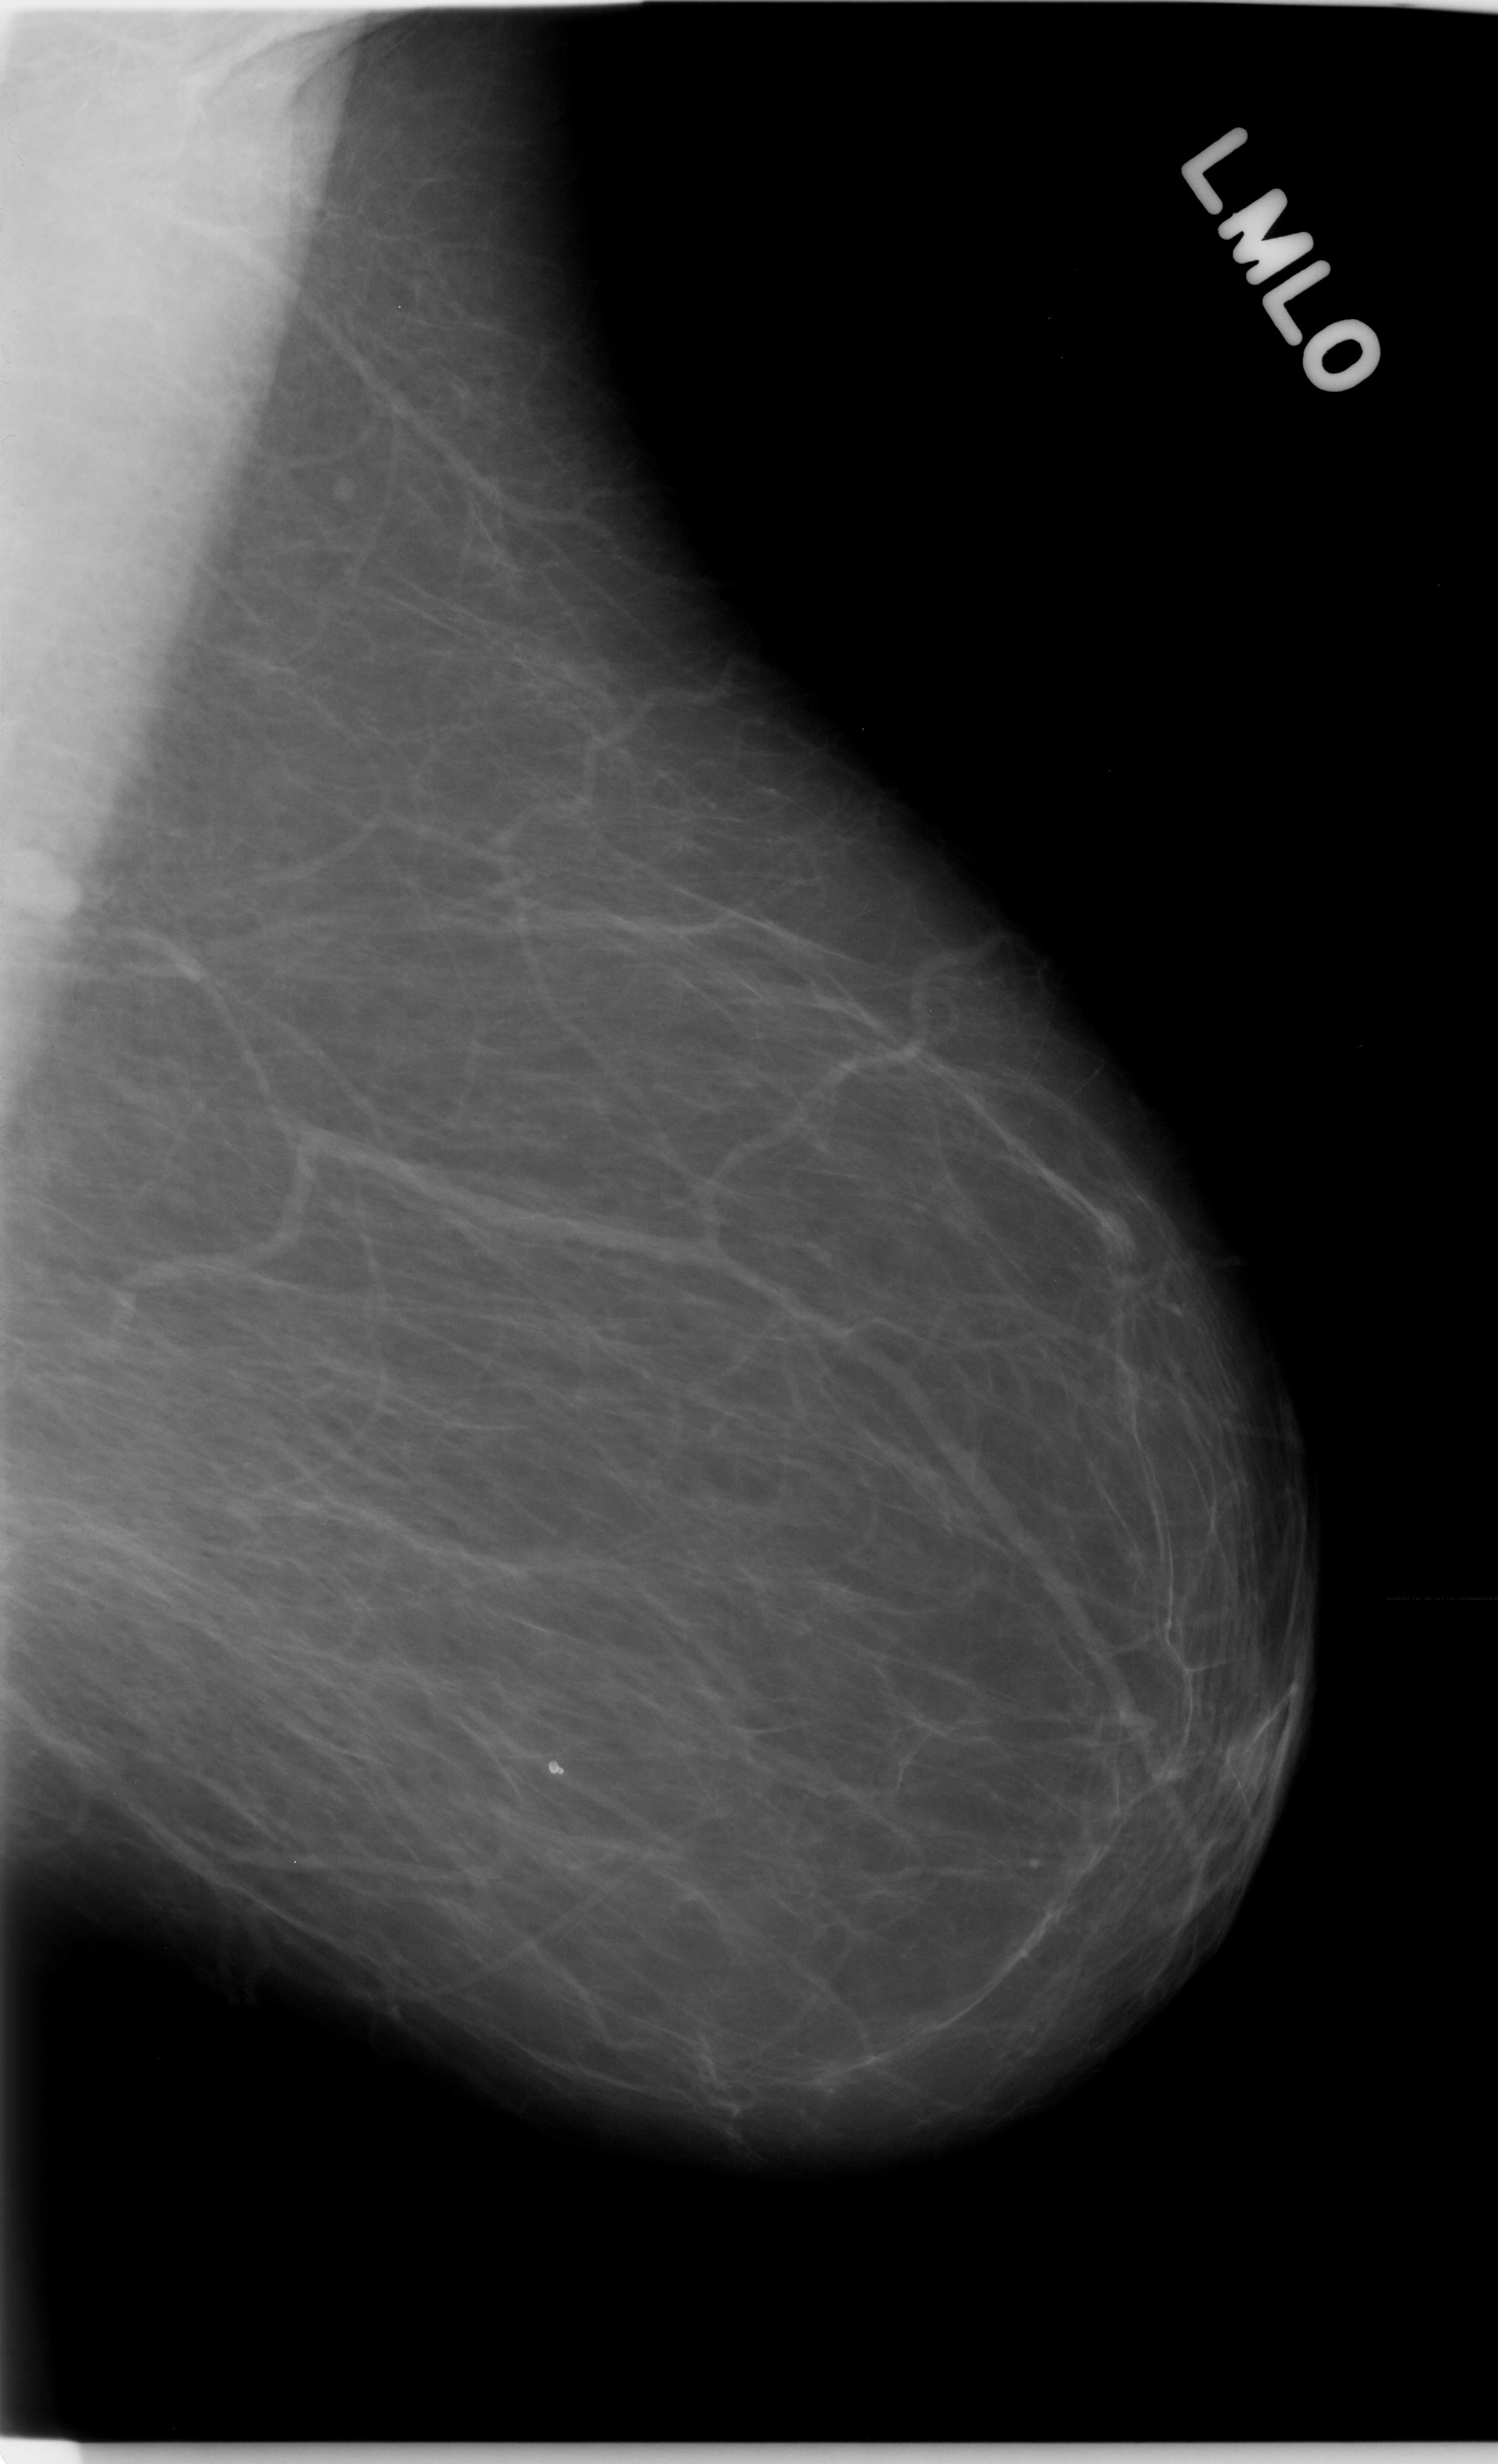
Mammogram (digitized film); left breast; MLO view; BI-RADS breast density category 1 (scale 1–4).
Finding: mass, shape oval, margins circumscribed; BI-RADS assessment category 4; subtlety rating 3 on a 1 (subtle) to 5 (obvious) scale; pathology (as recorded): malignant.